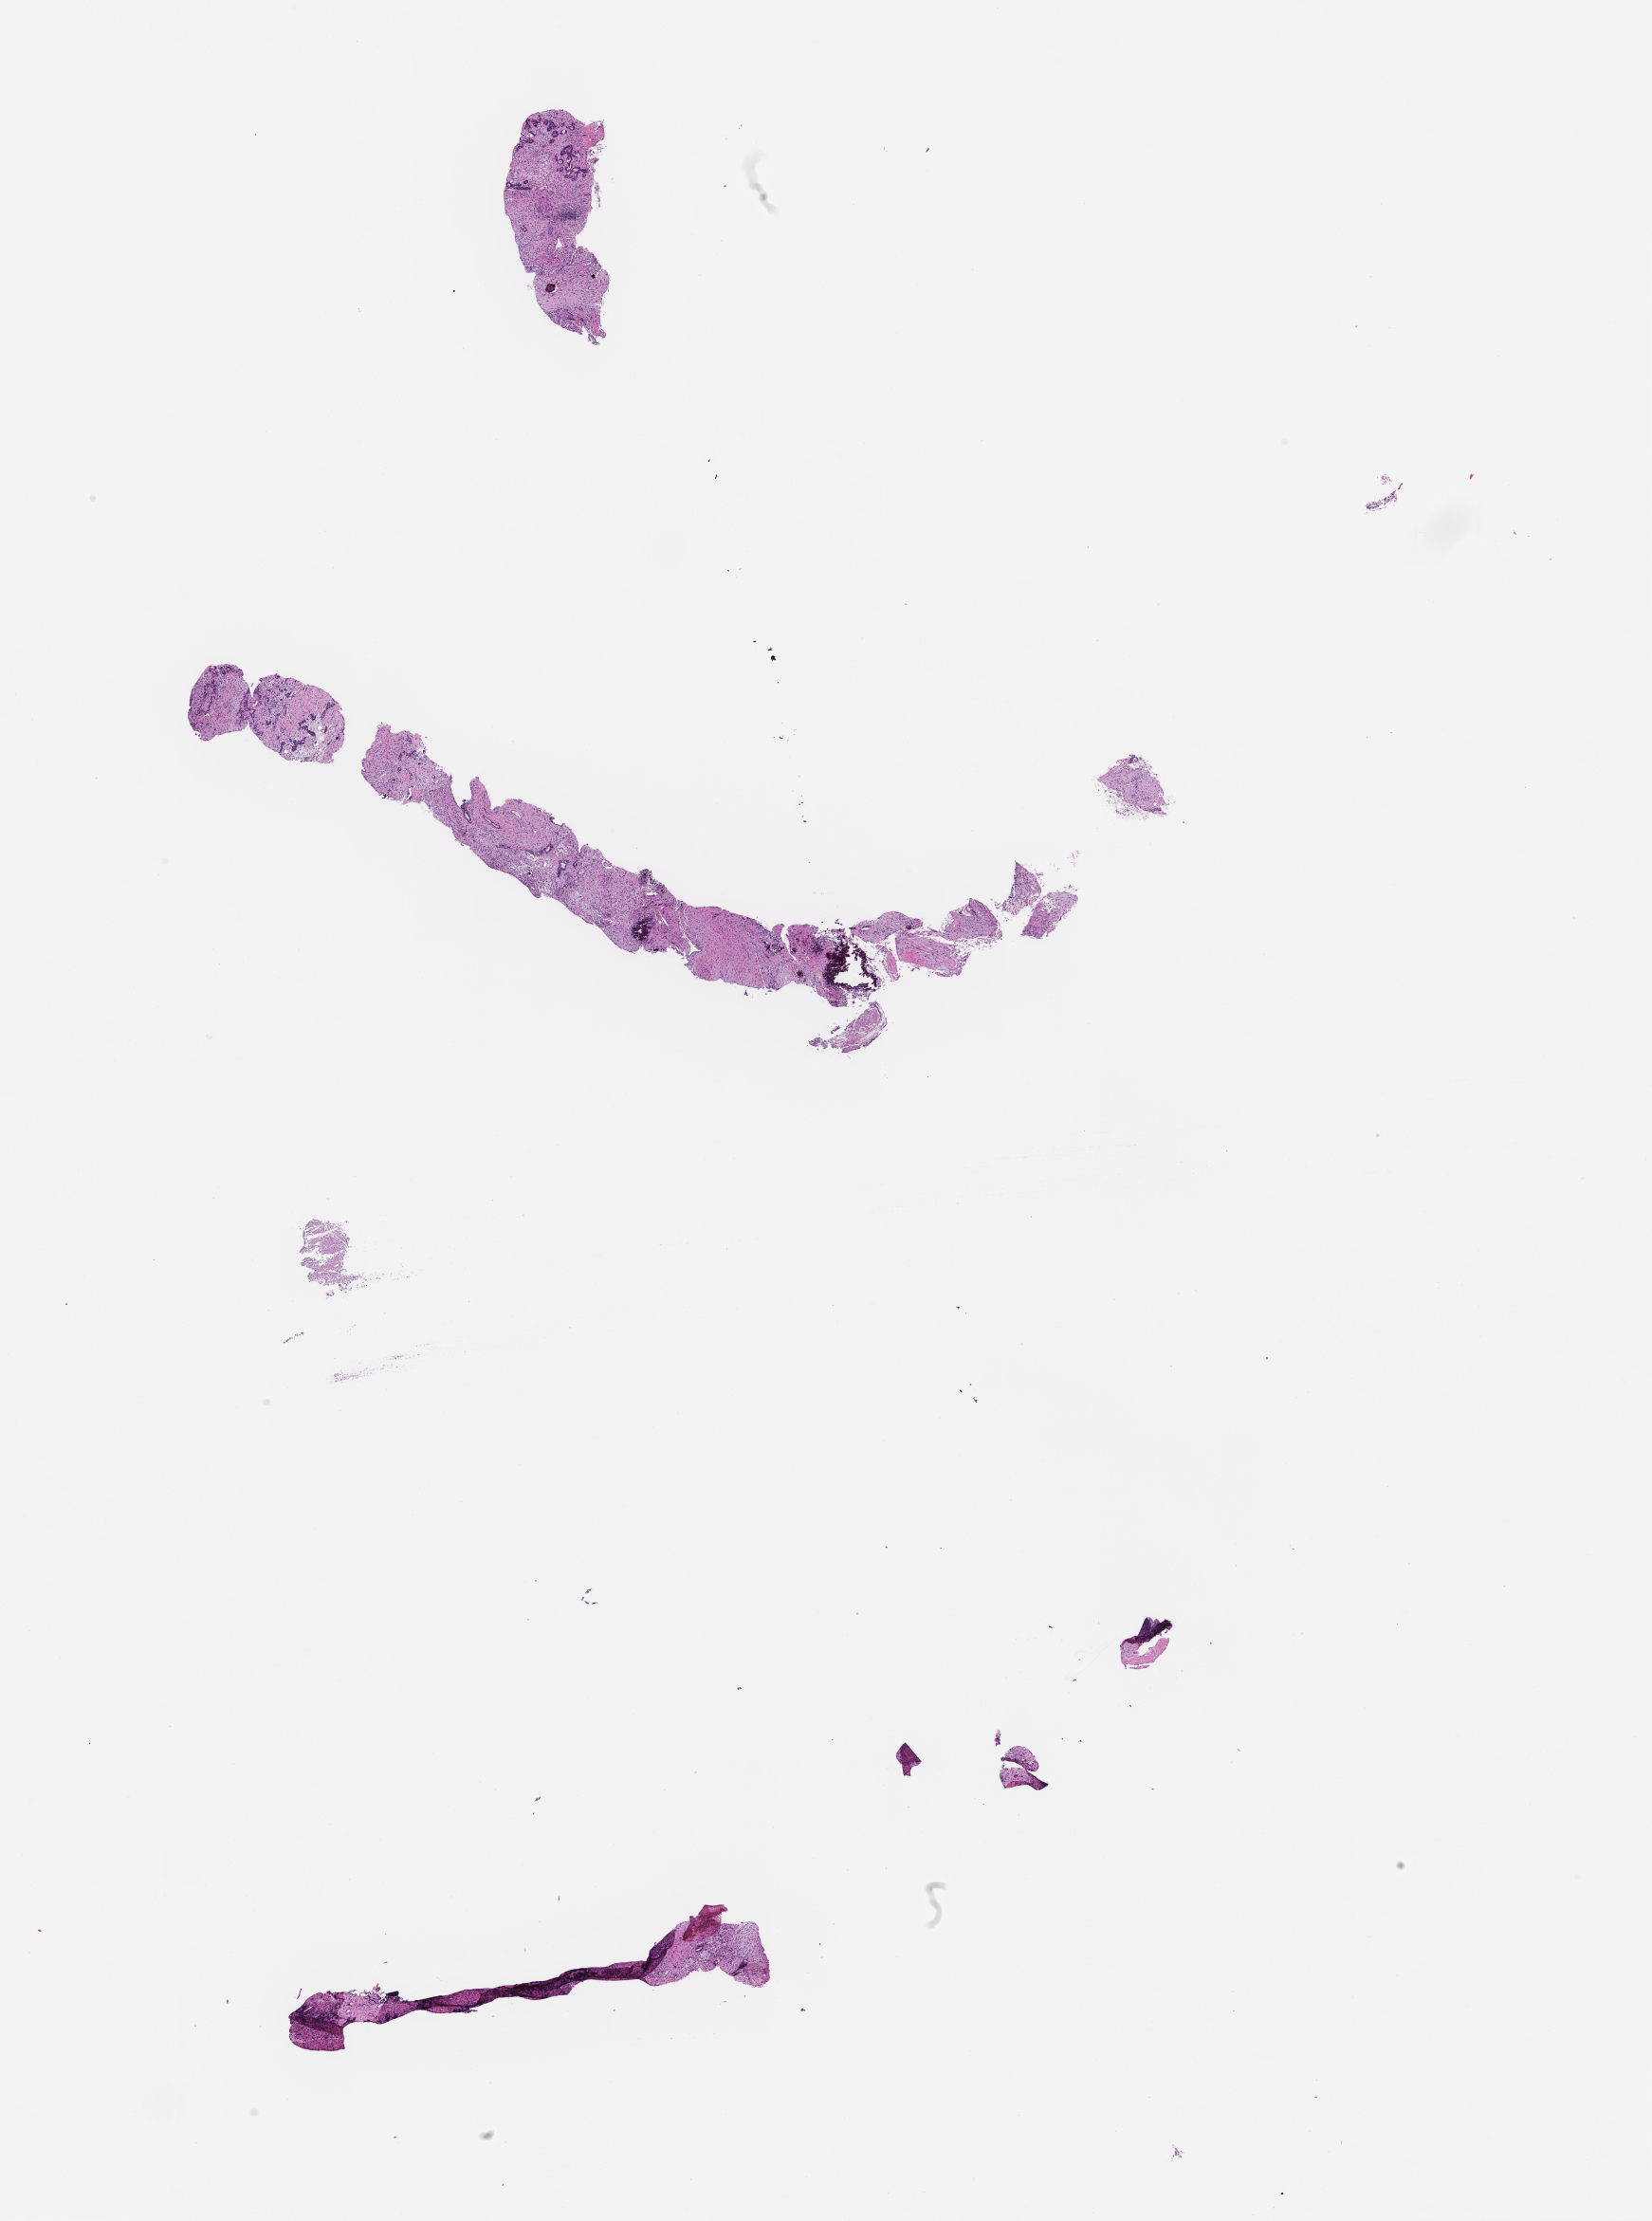
Whole-slide image, hematoxylin and eosin (H&E) stain — whole scanned area (about 14.1 x 18.9 mm) shown as a low-resolution overview, formalin-fixed, paraffin-embedded (FFPE) tissue. Patient: male.
This section: metastasis (sampled organ not recorded). Patient diagnosis (primary): Colorectal Carcinoma.